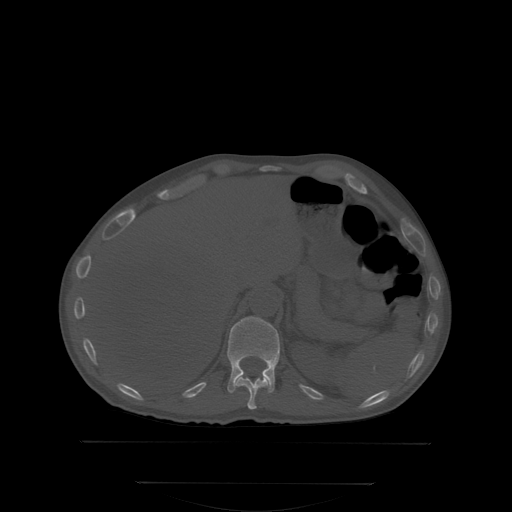
CT including the spine, one axial slice; bone window (W 1800 / L 400 HU); 2.5 mm slice thickness; 512 × 512 image matrix, field of view 500 × 500 mm. Patient: male, 58 years. Case-level facts recorded for this patient, not image findings: primary cancer: prostate; vertebrae with lytic lesions (as recorded): L1.
Outlined on this slice (semi-automatically segmented with operator editing):
- T11 vertebra: bounding box [x1, y1, x2, y2] px = [238, 377, 267, 408]
- T12 vertebra: [228, 316, 279, 392]